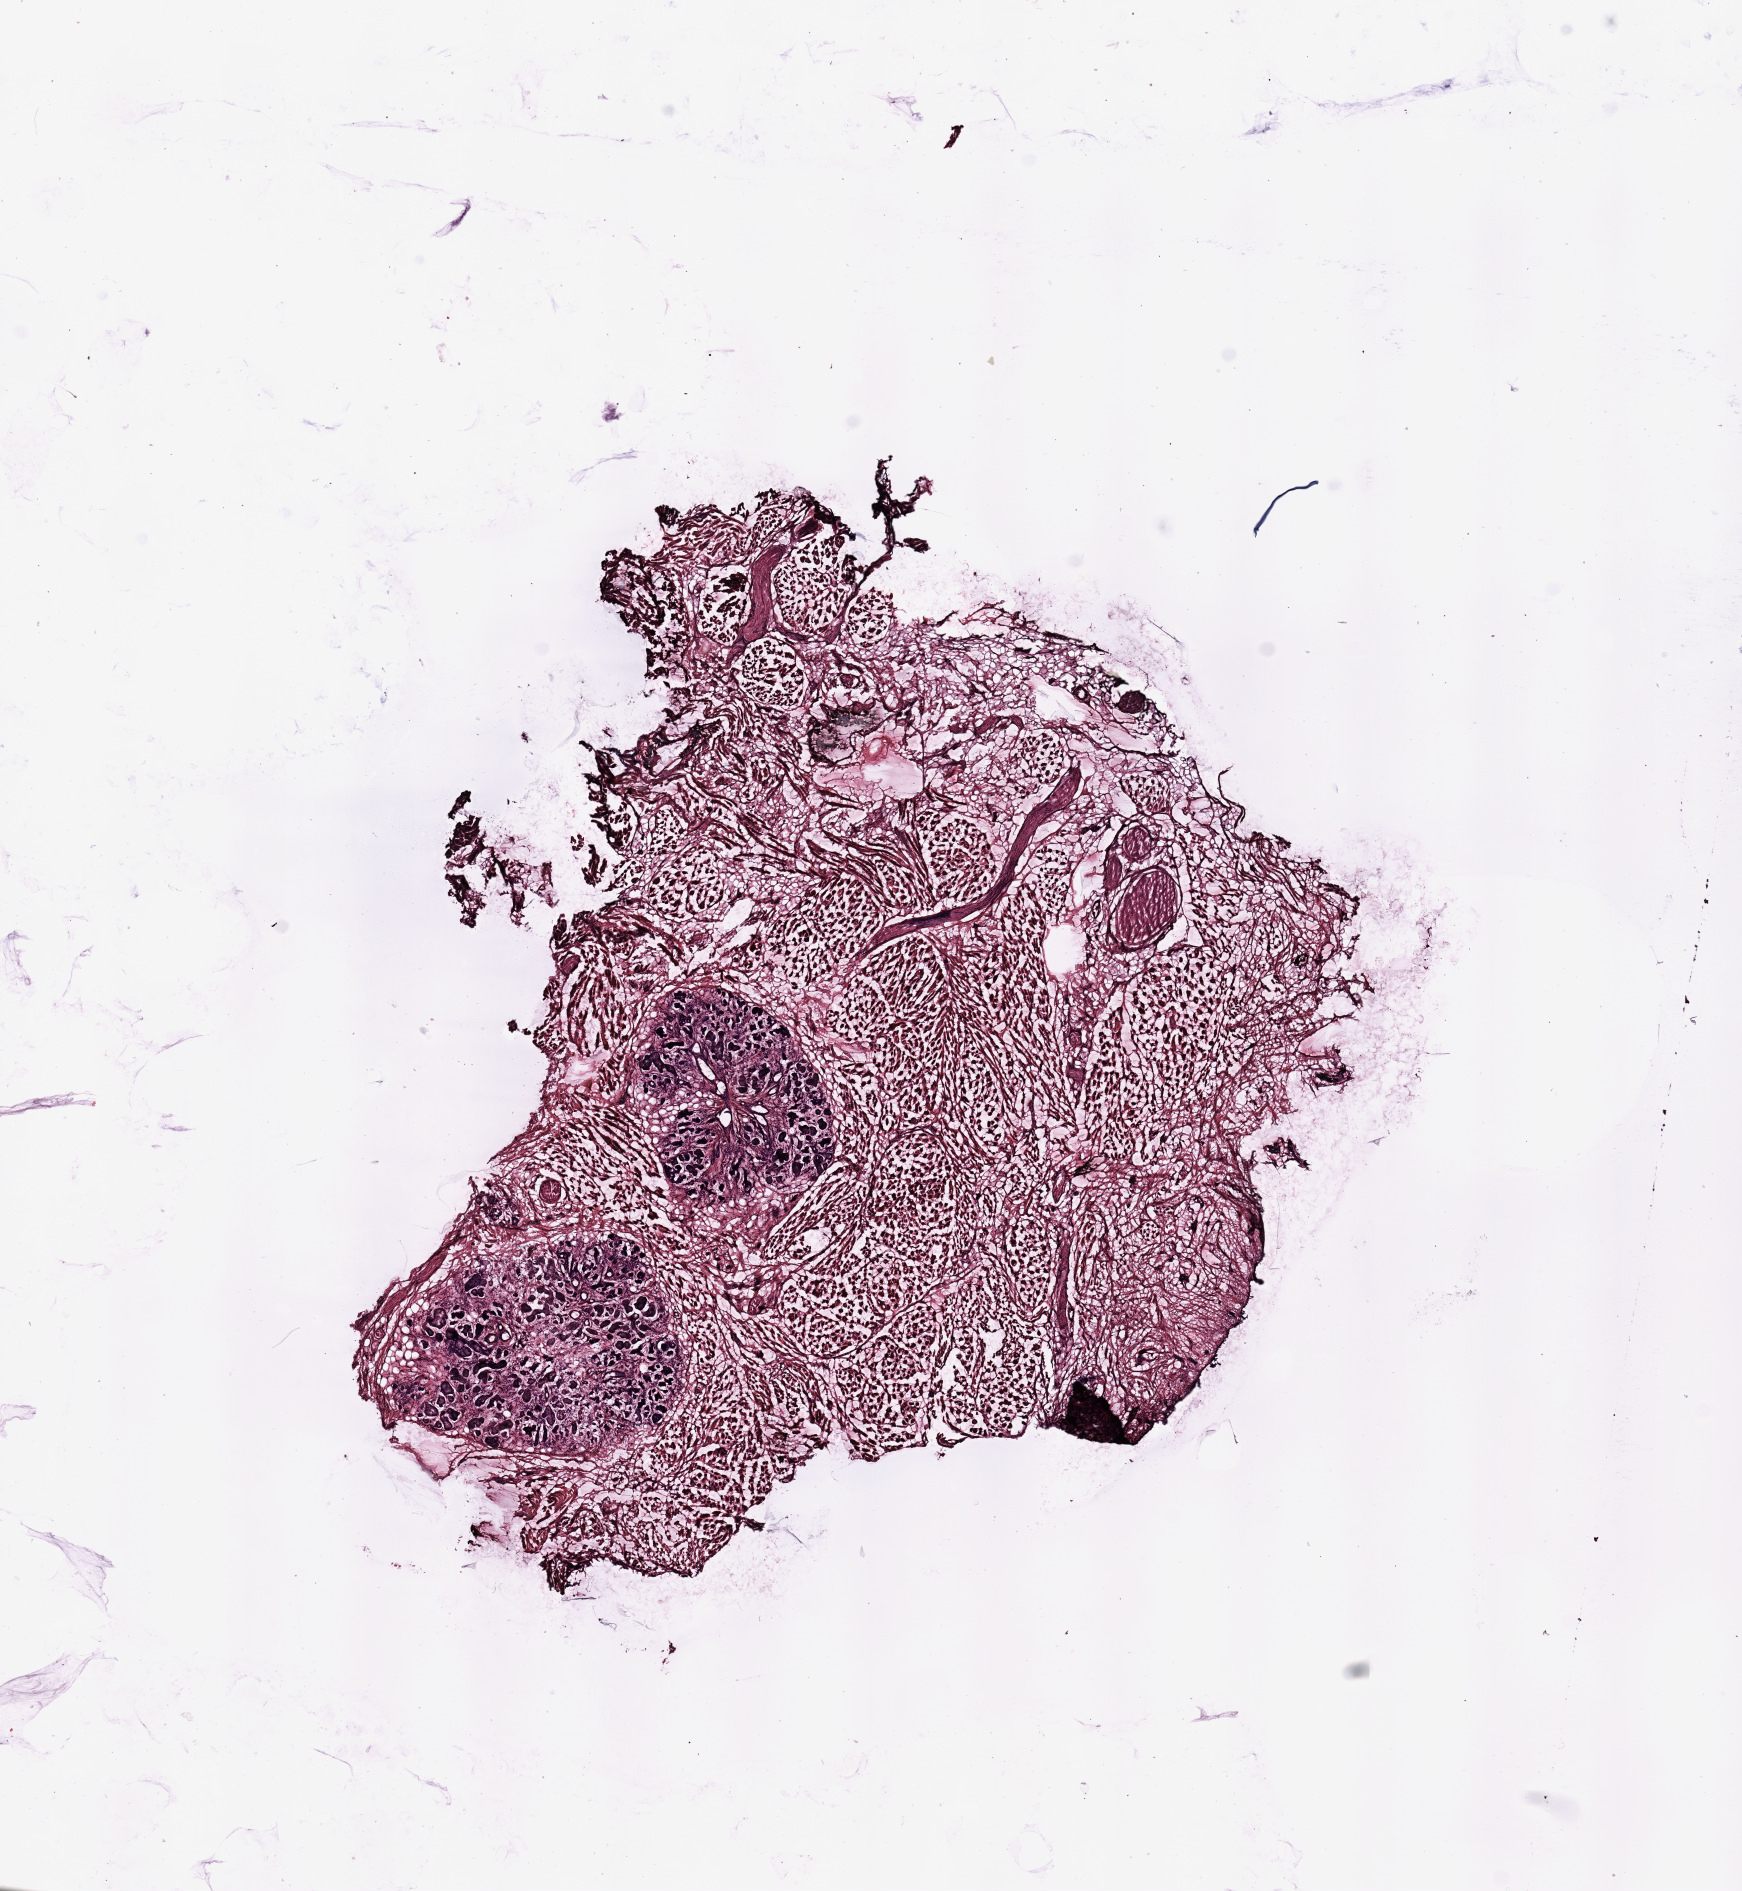
H&E whole-slide image — low-resolution overview of the scanned area, about 13.8 x 15.0 mm (acquisition: 20x scan). Head and neck, tissue type not recorded. Patient: male, age 67 years.
- patient diagnosis: Squamous cell carcinoma, NOS (tongue, NOS)